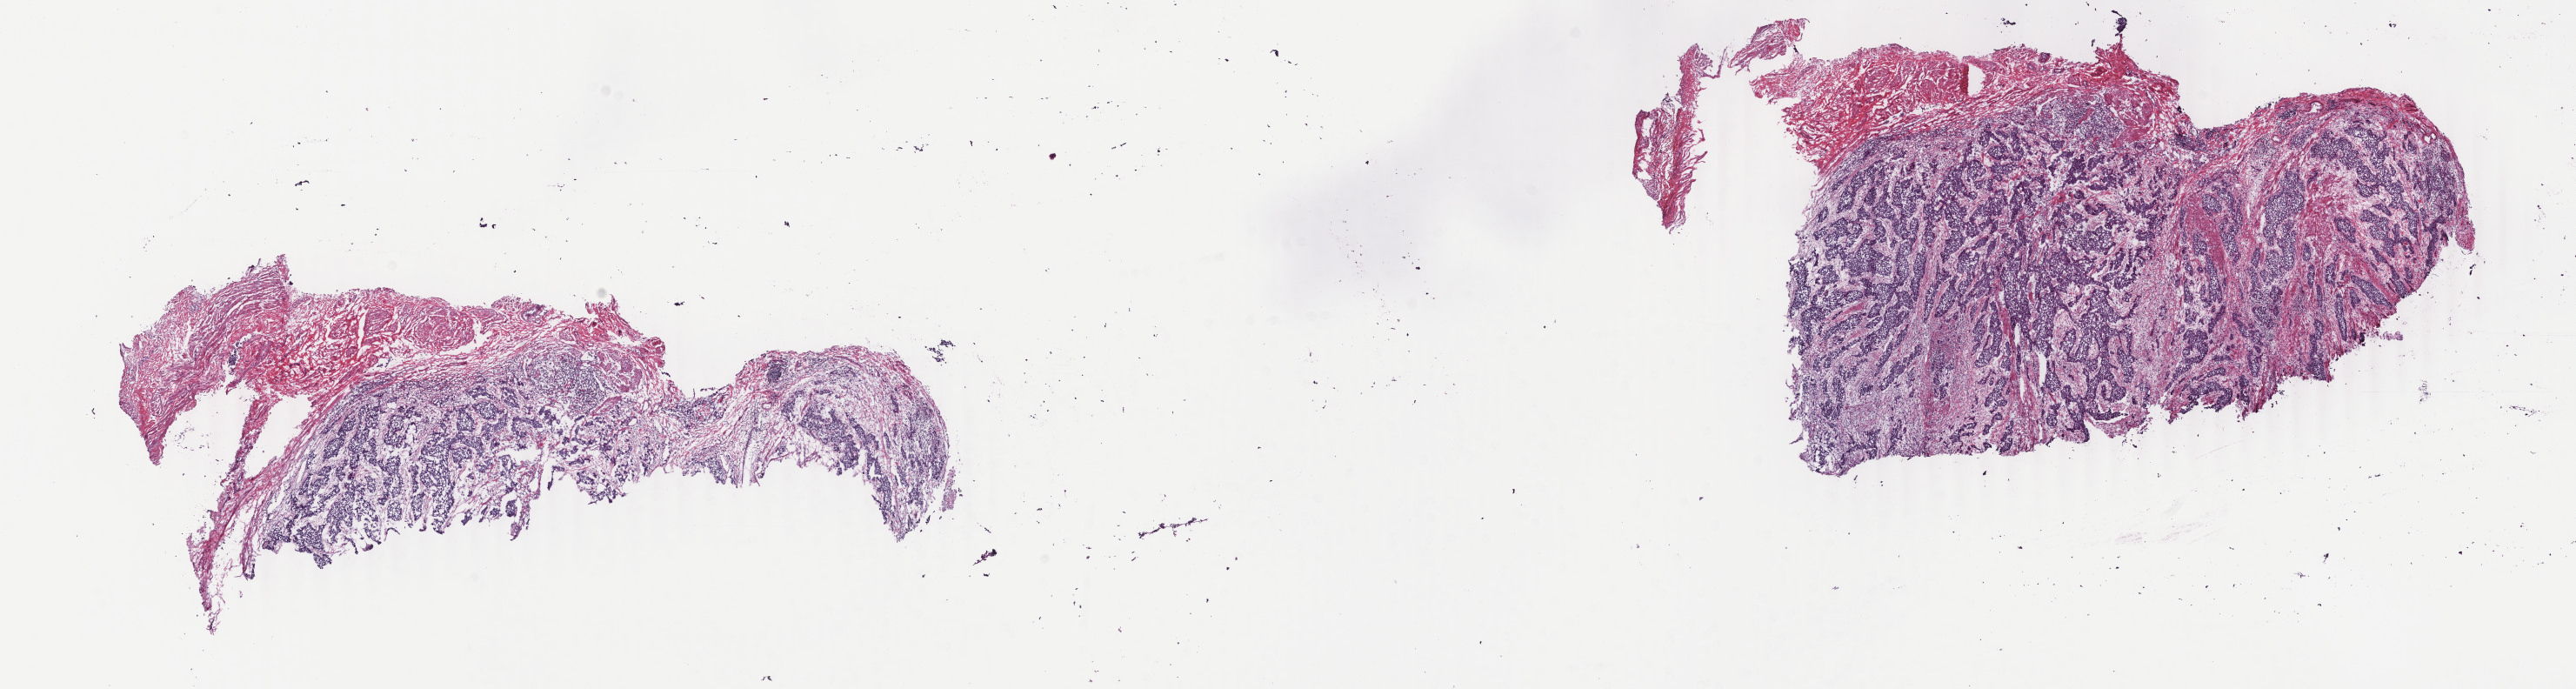
H&E whole-slide image — whole scanned area (about 23.6 x 6.3 mm, acquisition: 40x scan) shown as a low-resolution overview, frozen section from the top of the tissue portion, sample: primary tumour, bladder. Male, age 69 years at initial diagnosis. Histologic grade: high grade. Pathologist review of this section (percent, as recorded): tumour cells 80%, tumour nuclei 80%, normal cells 0%, stromal cells 20%, necrosis 0%. Inflammatory infiltration, as recorded: lymphocyte infiltration 2%, monocyte infiltration 1%, neutrophil infiltration 1%.
Pathologic diagnosis: Transitional cell carcinoma. AJCC pathologic stage: IV (5th edition). Lymph nodes positive (case pathology): 2 of 14 examined.